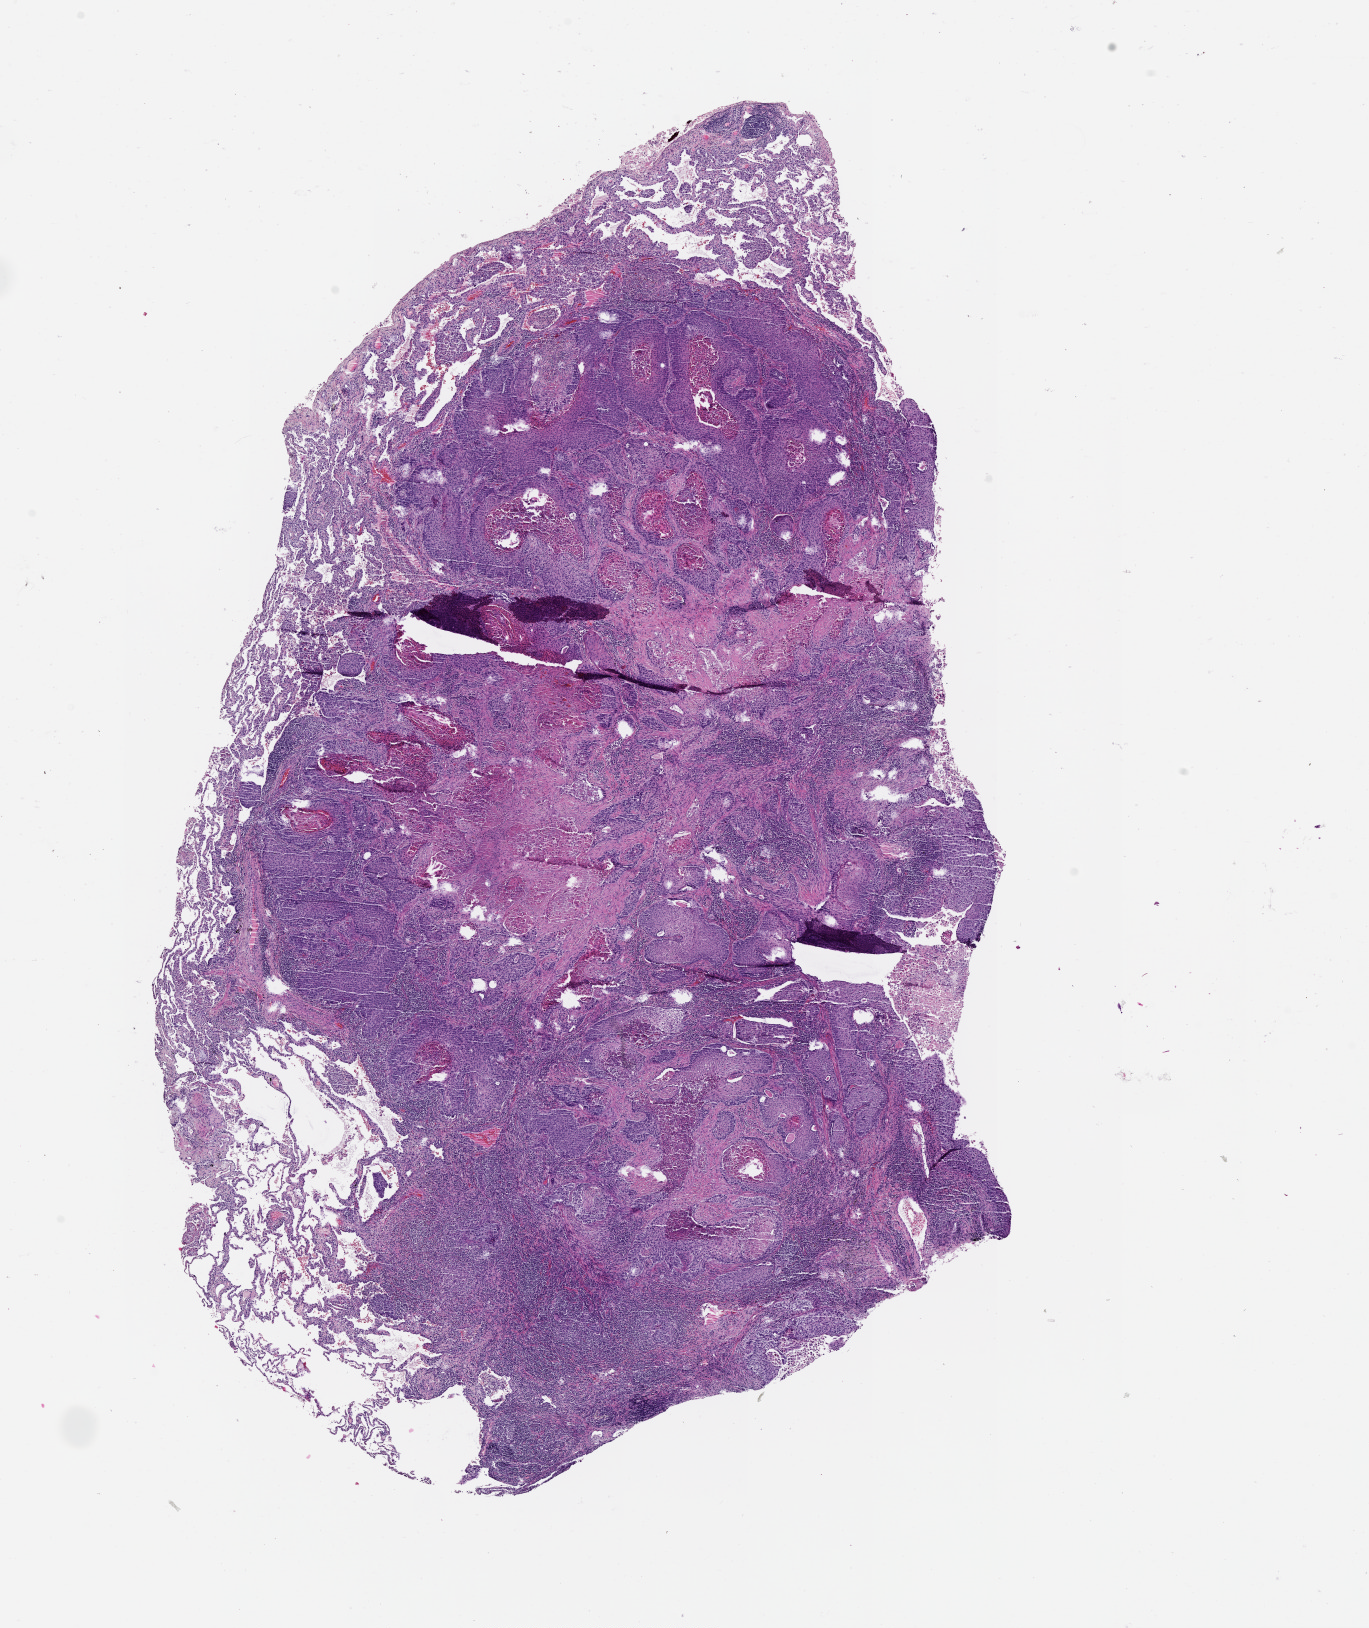
Hematoxylin and eosin (H&E) stained whole-slide image — whole scanned area (about 11.0 x 13.1 mm, acquisition: 20x scan) shown as a low-resolution overview; lung, tumour tissue. 67-year-old male patient.
Patient diagnosis (cohort enrolment): squamous cell carcinoma (lung).